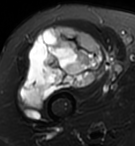
MRI of an extremity soft-tissue mass, one axial slice. Position 67 of 95 along the scan axis. T2-weighted fat-saturated. MR volume resampled by the dataset authors to the PET/CT grid (not the native acquisition matrix). 135 × 146 image matrix, field of view 132 × 143 mm. Female patient. Case-level facts recorded for this patient, not image findings: histological type: pleiomorphic undifferentiated sarcoma; grade: high; site of the primary tumour: right quadricep.
Structures marked on this image (expert contour drawn on MRI and transferred to this co-registered scan by the dataset authors):
- gross tumour volume including surrounding oedema: bounding box [x1, y1, x2, y2] px = [21, 25, 107, 110]
- gross tumour volume (mass): [21, 25, 107, 110]